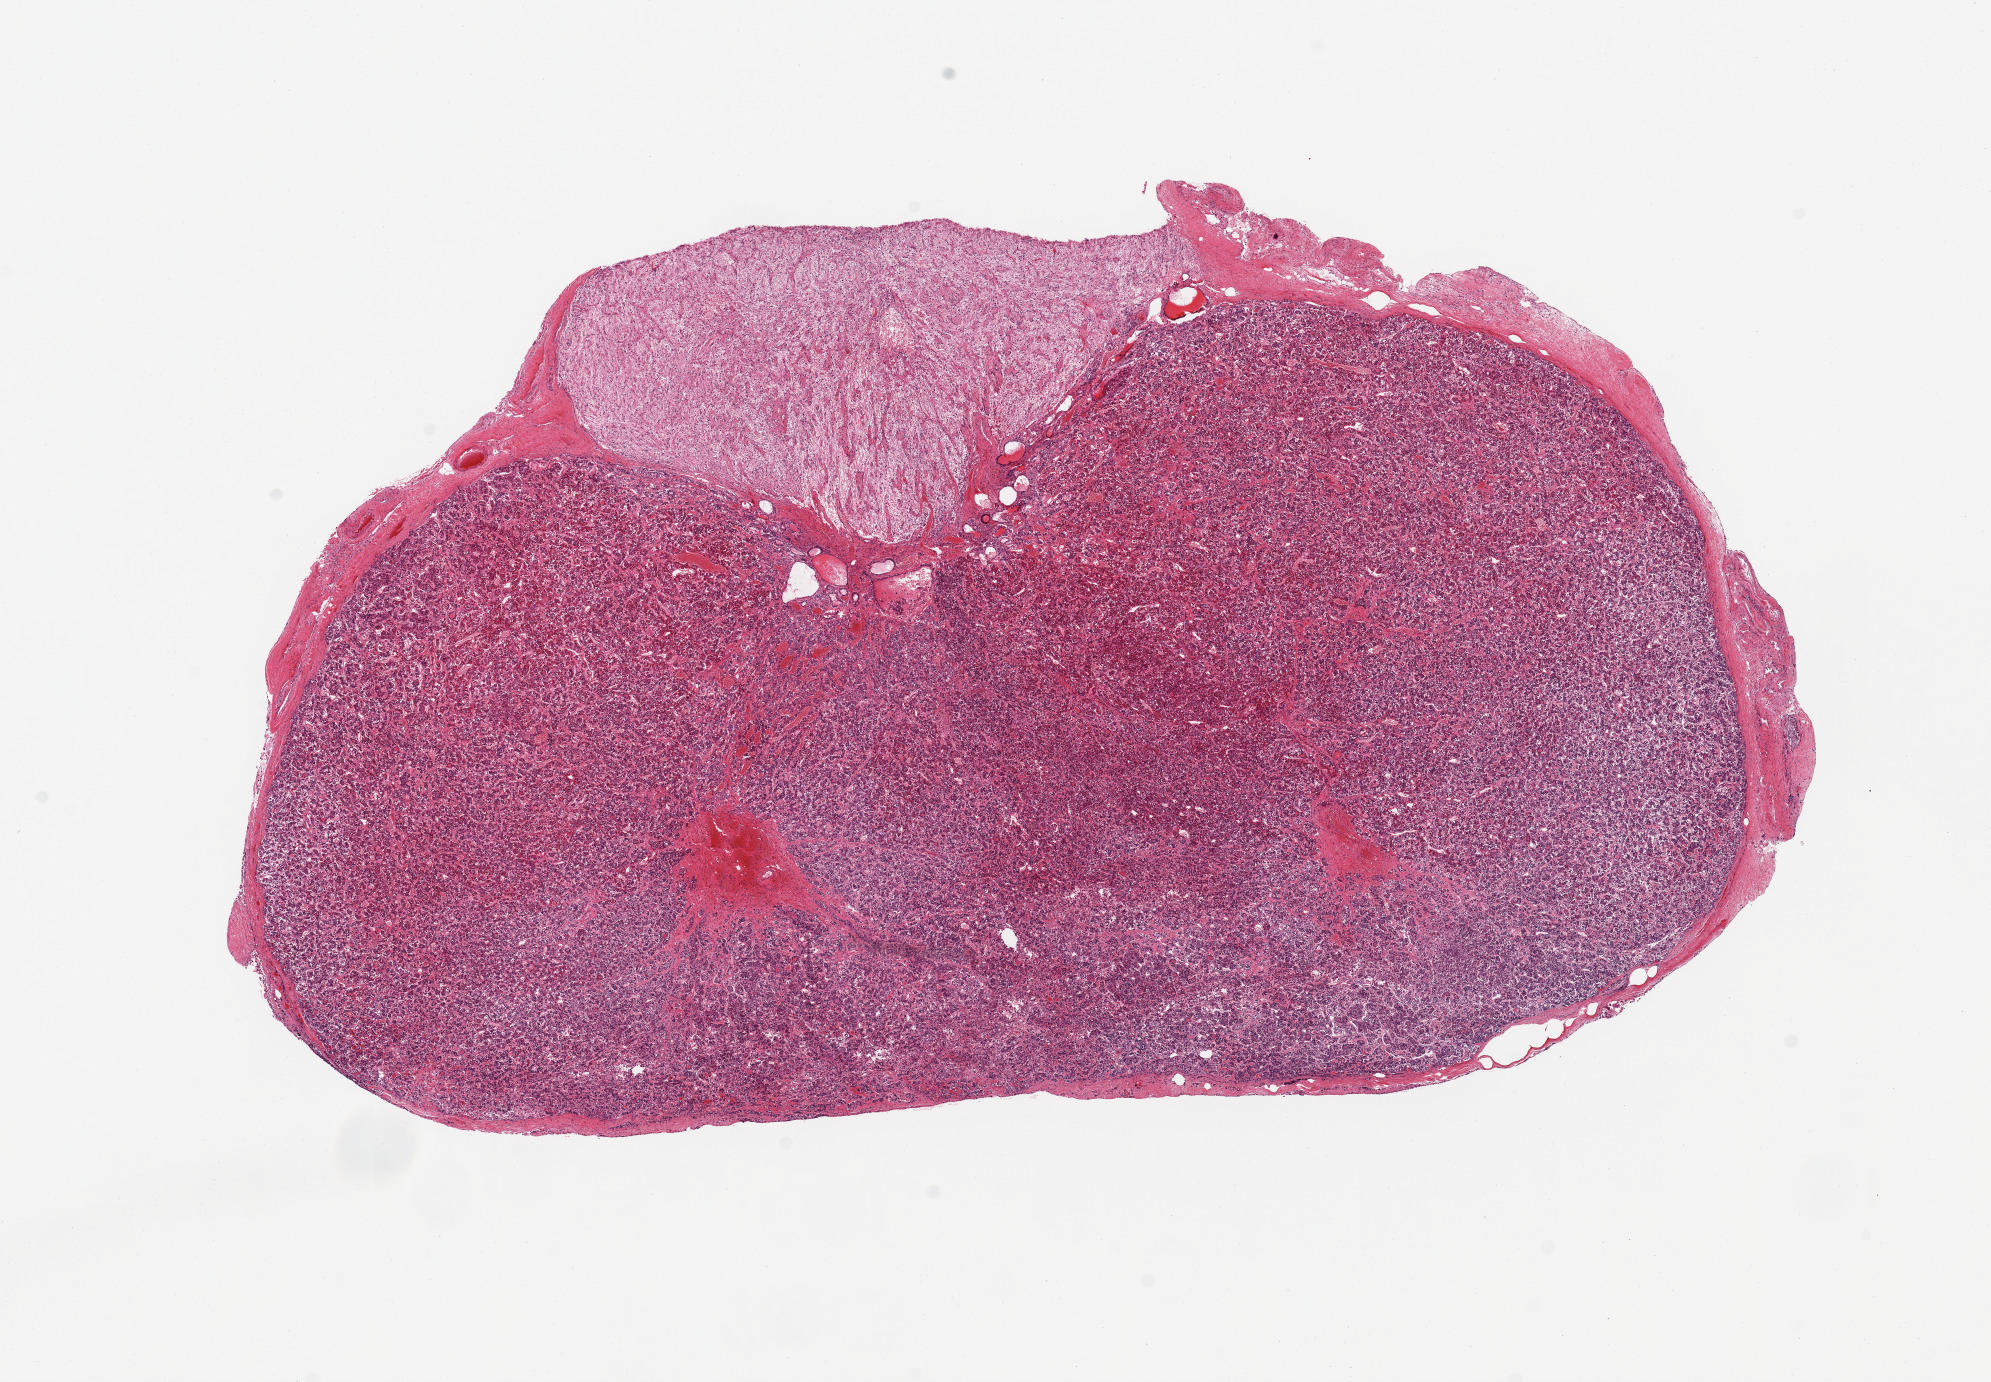
Whole-slide image, haematoxylin and eosin stain, whole scanned area (about 15.8 x 10.9 mm, slide scanned at 20x) shown as a low-resolution overview. PAXgene-fixed paraffin-embedded (PFPE) section. Target tissue: pituitary. Donor tissue sample. Donor: male.
- pathologist's review note for this sample: 1 piece, autolysis approached score 2; 5x2 focus of neurohypophysis; rest is adenohypophysis